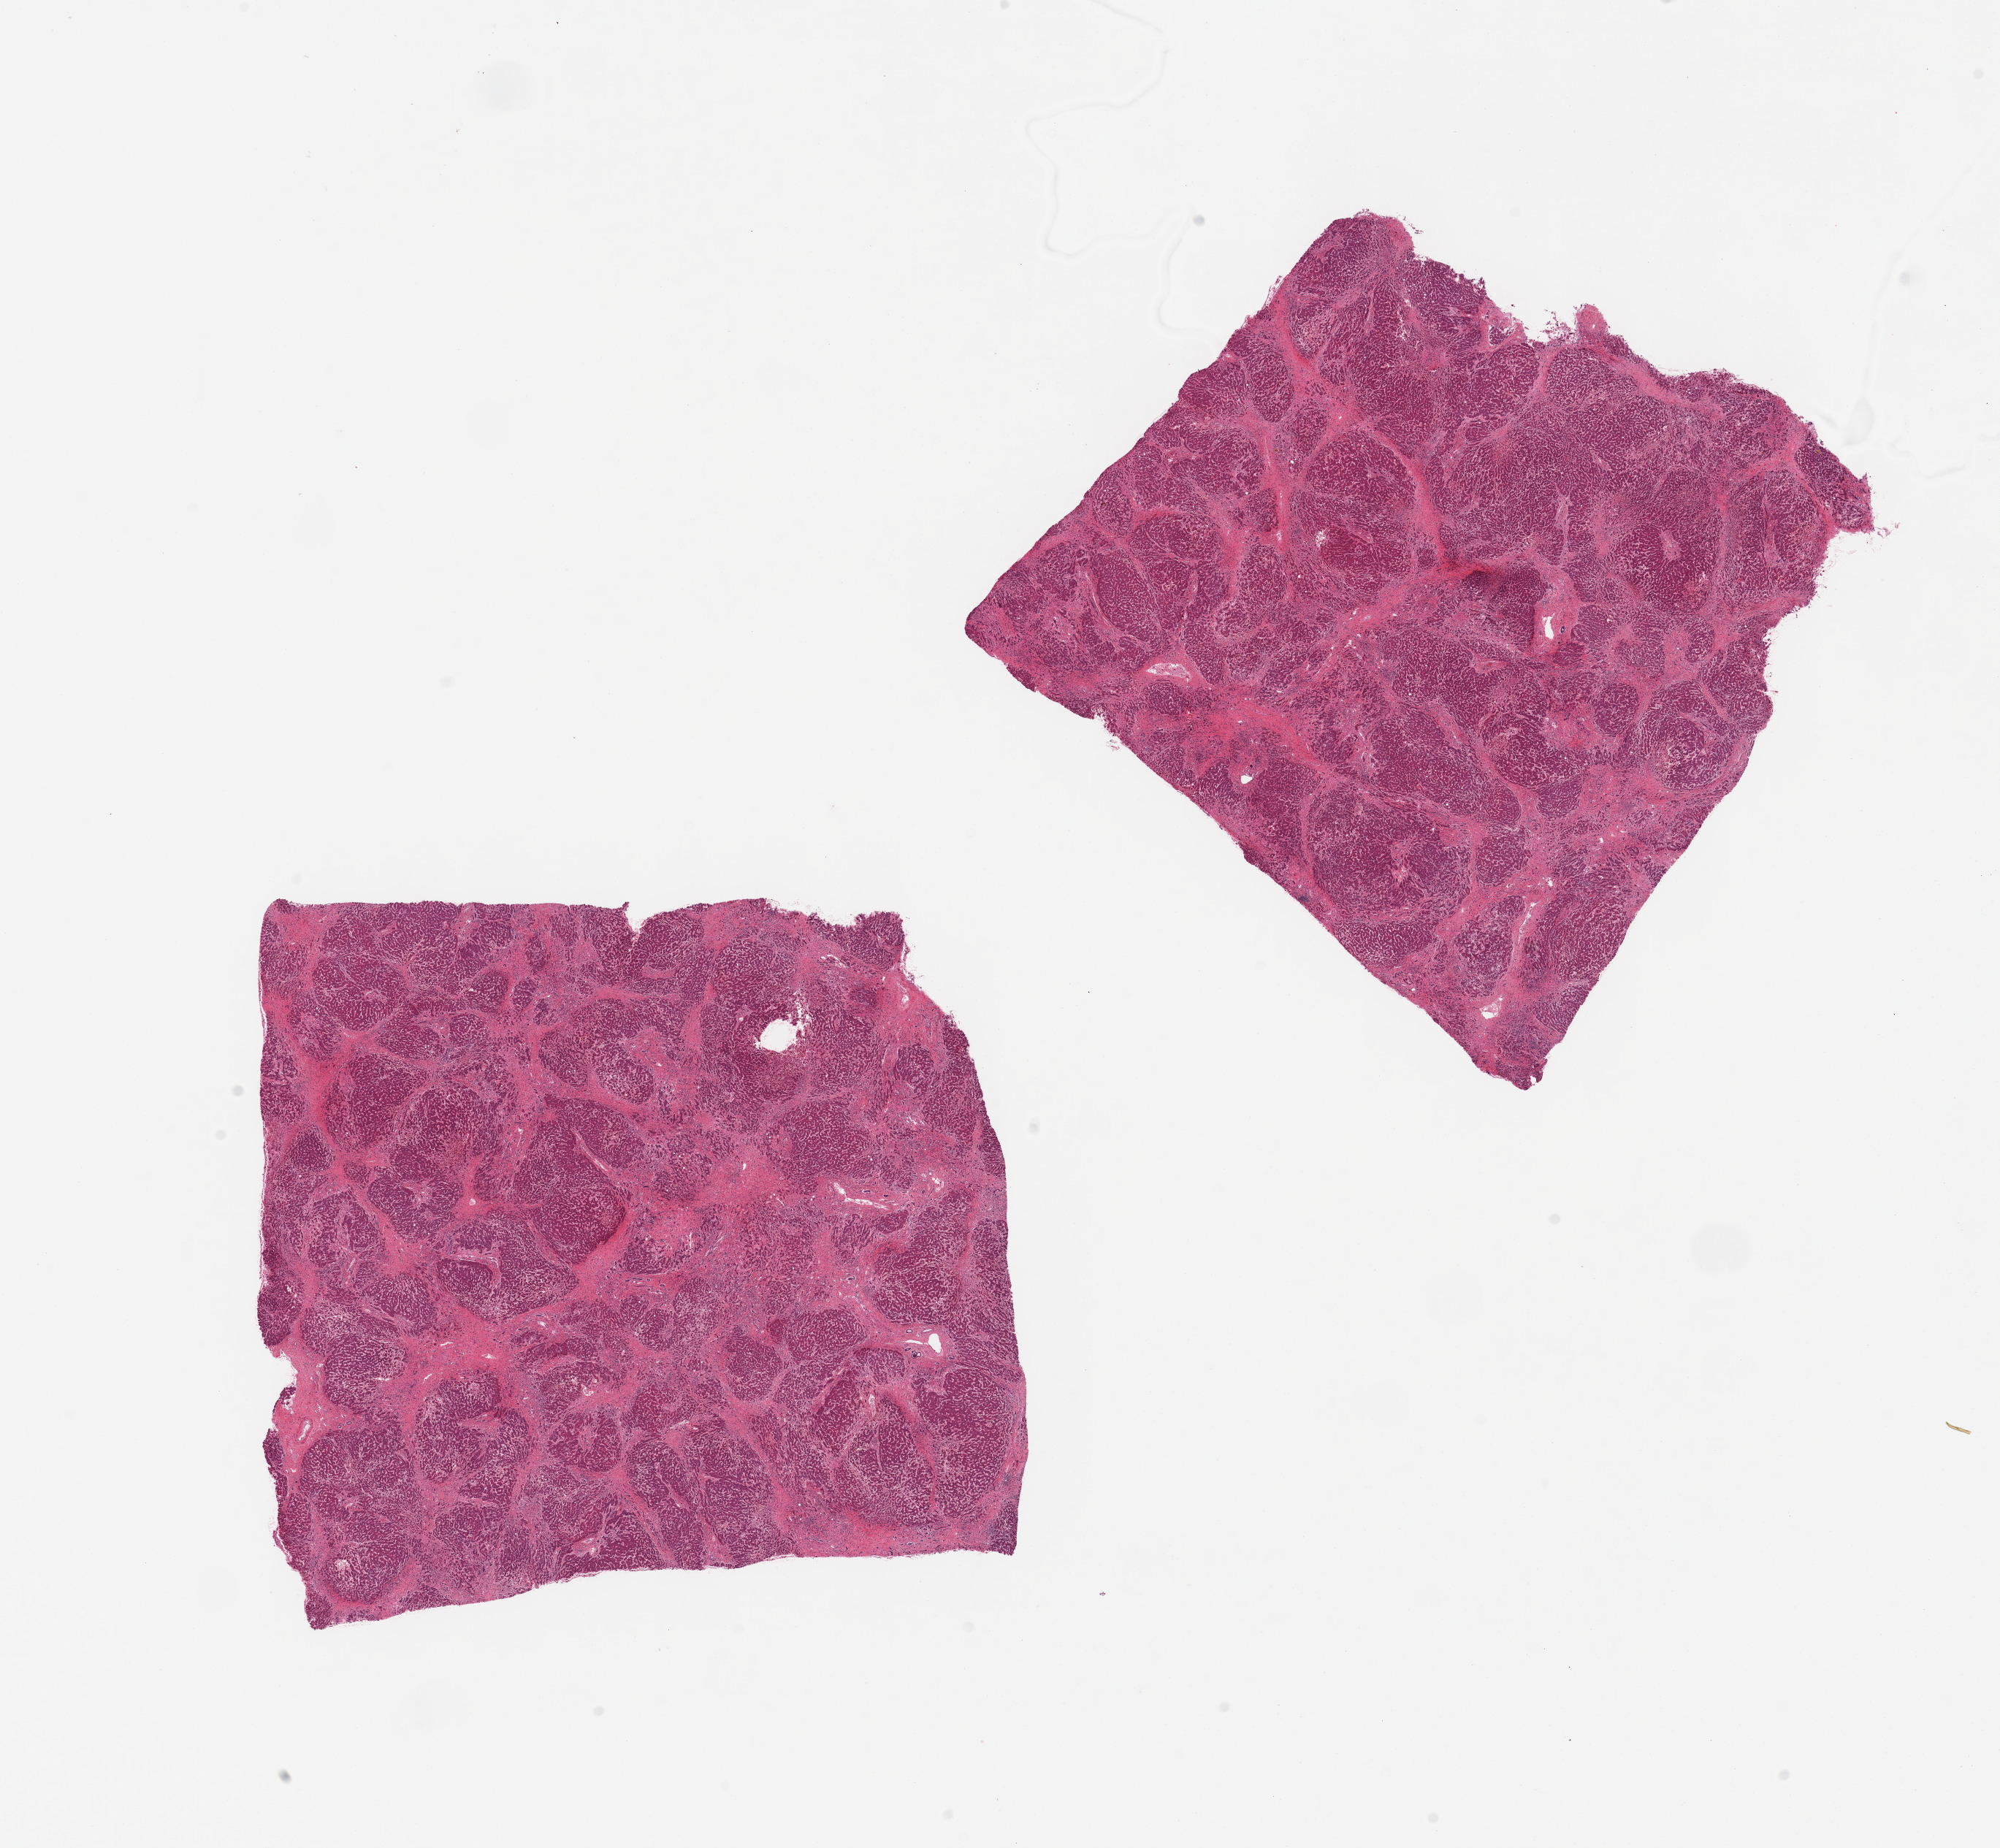
Haematoxylin and eosin whole-slide image, brightfield — low-resolution overview of the scanned area, about 21.7 x 20.0 mm (acquisition: 20x scan). PAXgene-fixed paraffin-embedded (PFPE) section. Target tissue: liver. Tissue donor sample.
Review note (as recorded): 2 pieces; cirrhosis, cholestatic features.